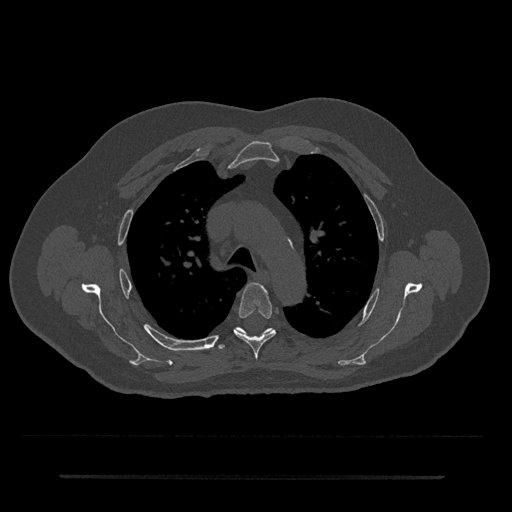
CT including the spine, one axial slice; position 519 of 797 along the scan axis; reconstruction kernel Br40s/3; 120 kVp; bone window (W 1800 / L 400 HU); 0.5 mm slice thickness; 512 × 512 image matrix. Patient: male, 69 years. Case-level facts recorded for this patient, not image findings: primary cancer: prostate.
Structures marked on this image (semi-automatically segmented with operator editing):
- T4 vertebra: bounding box <234,283,276,360> (left, top, right, bottom; pixels)
- T5 vertebra: <218,327,274,349>